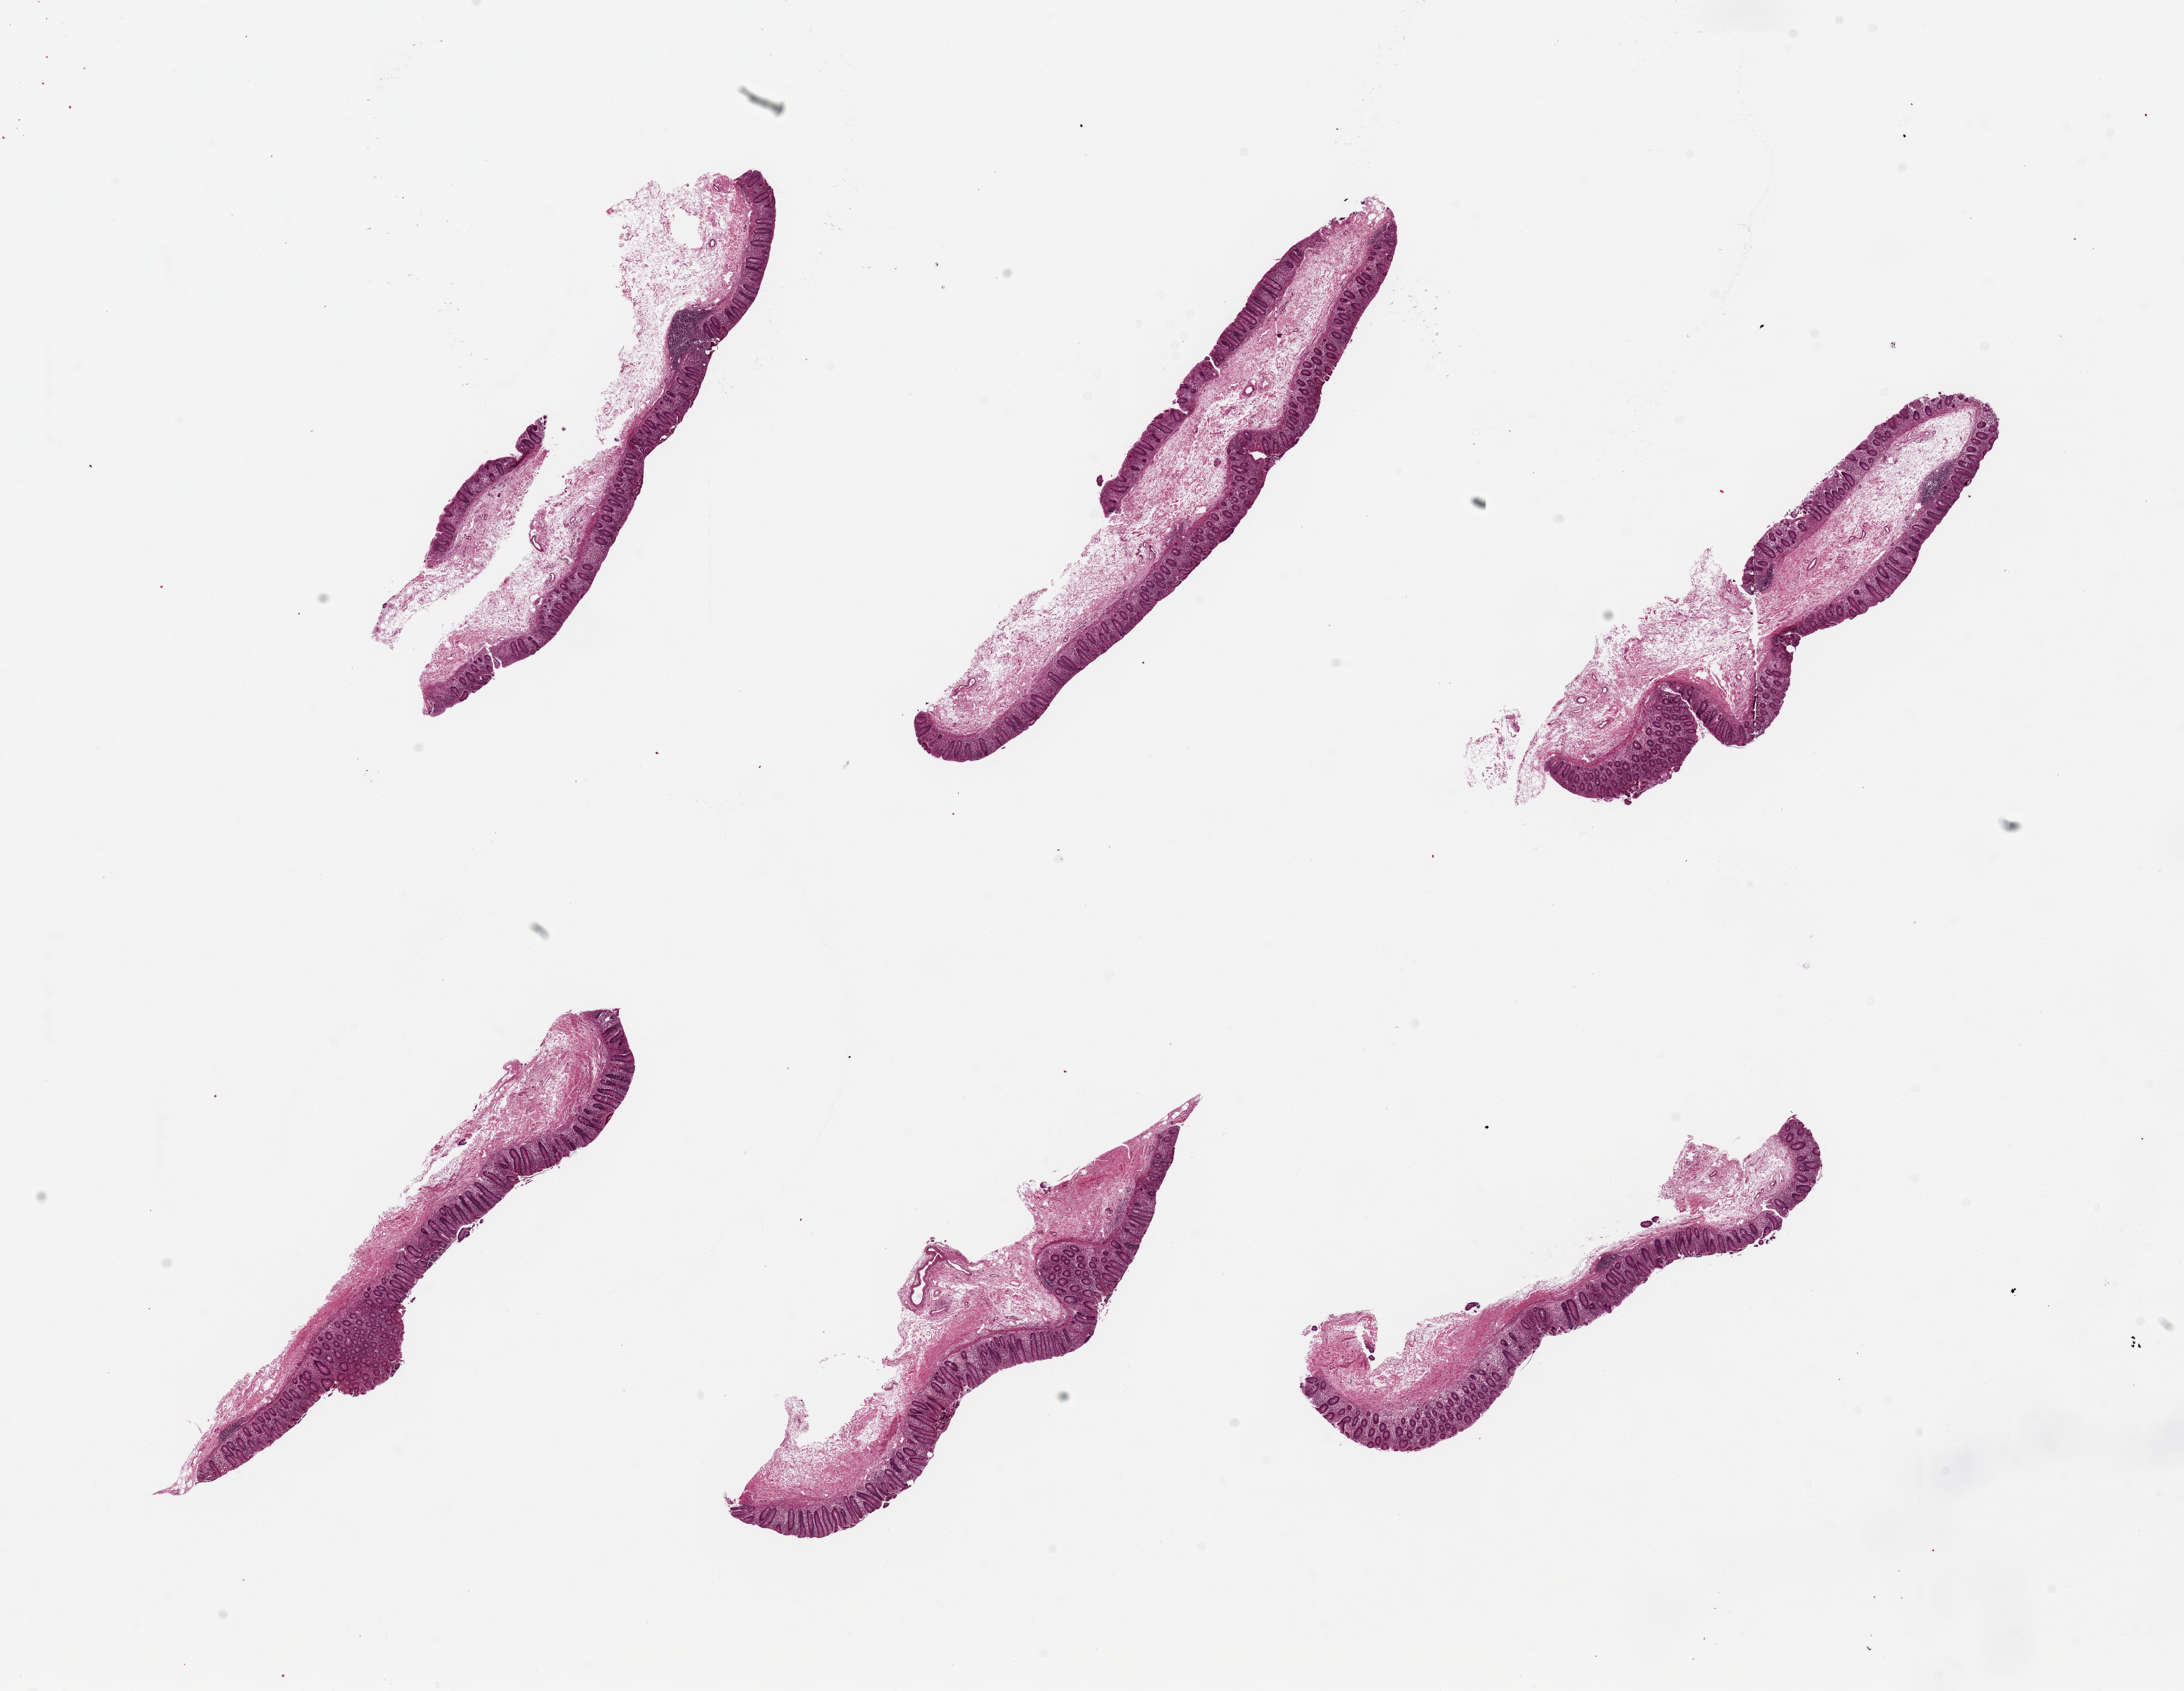
Digitized H&E-stained section, a low-resolution overview of the entire scanned area, about 24.6 x 19.1 mm; PAXgene-fixed, paraffin-embedded tissue; sampled site (target tissue): transverse colon; donor tissue sample. Donor sex: female.
Pathologist's review note for this sample: 6 pieces, up to 8x1.5mm; mucosa partially sloughed.